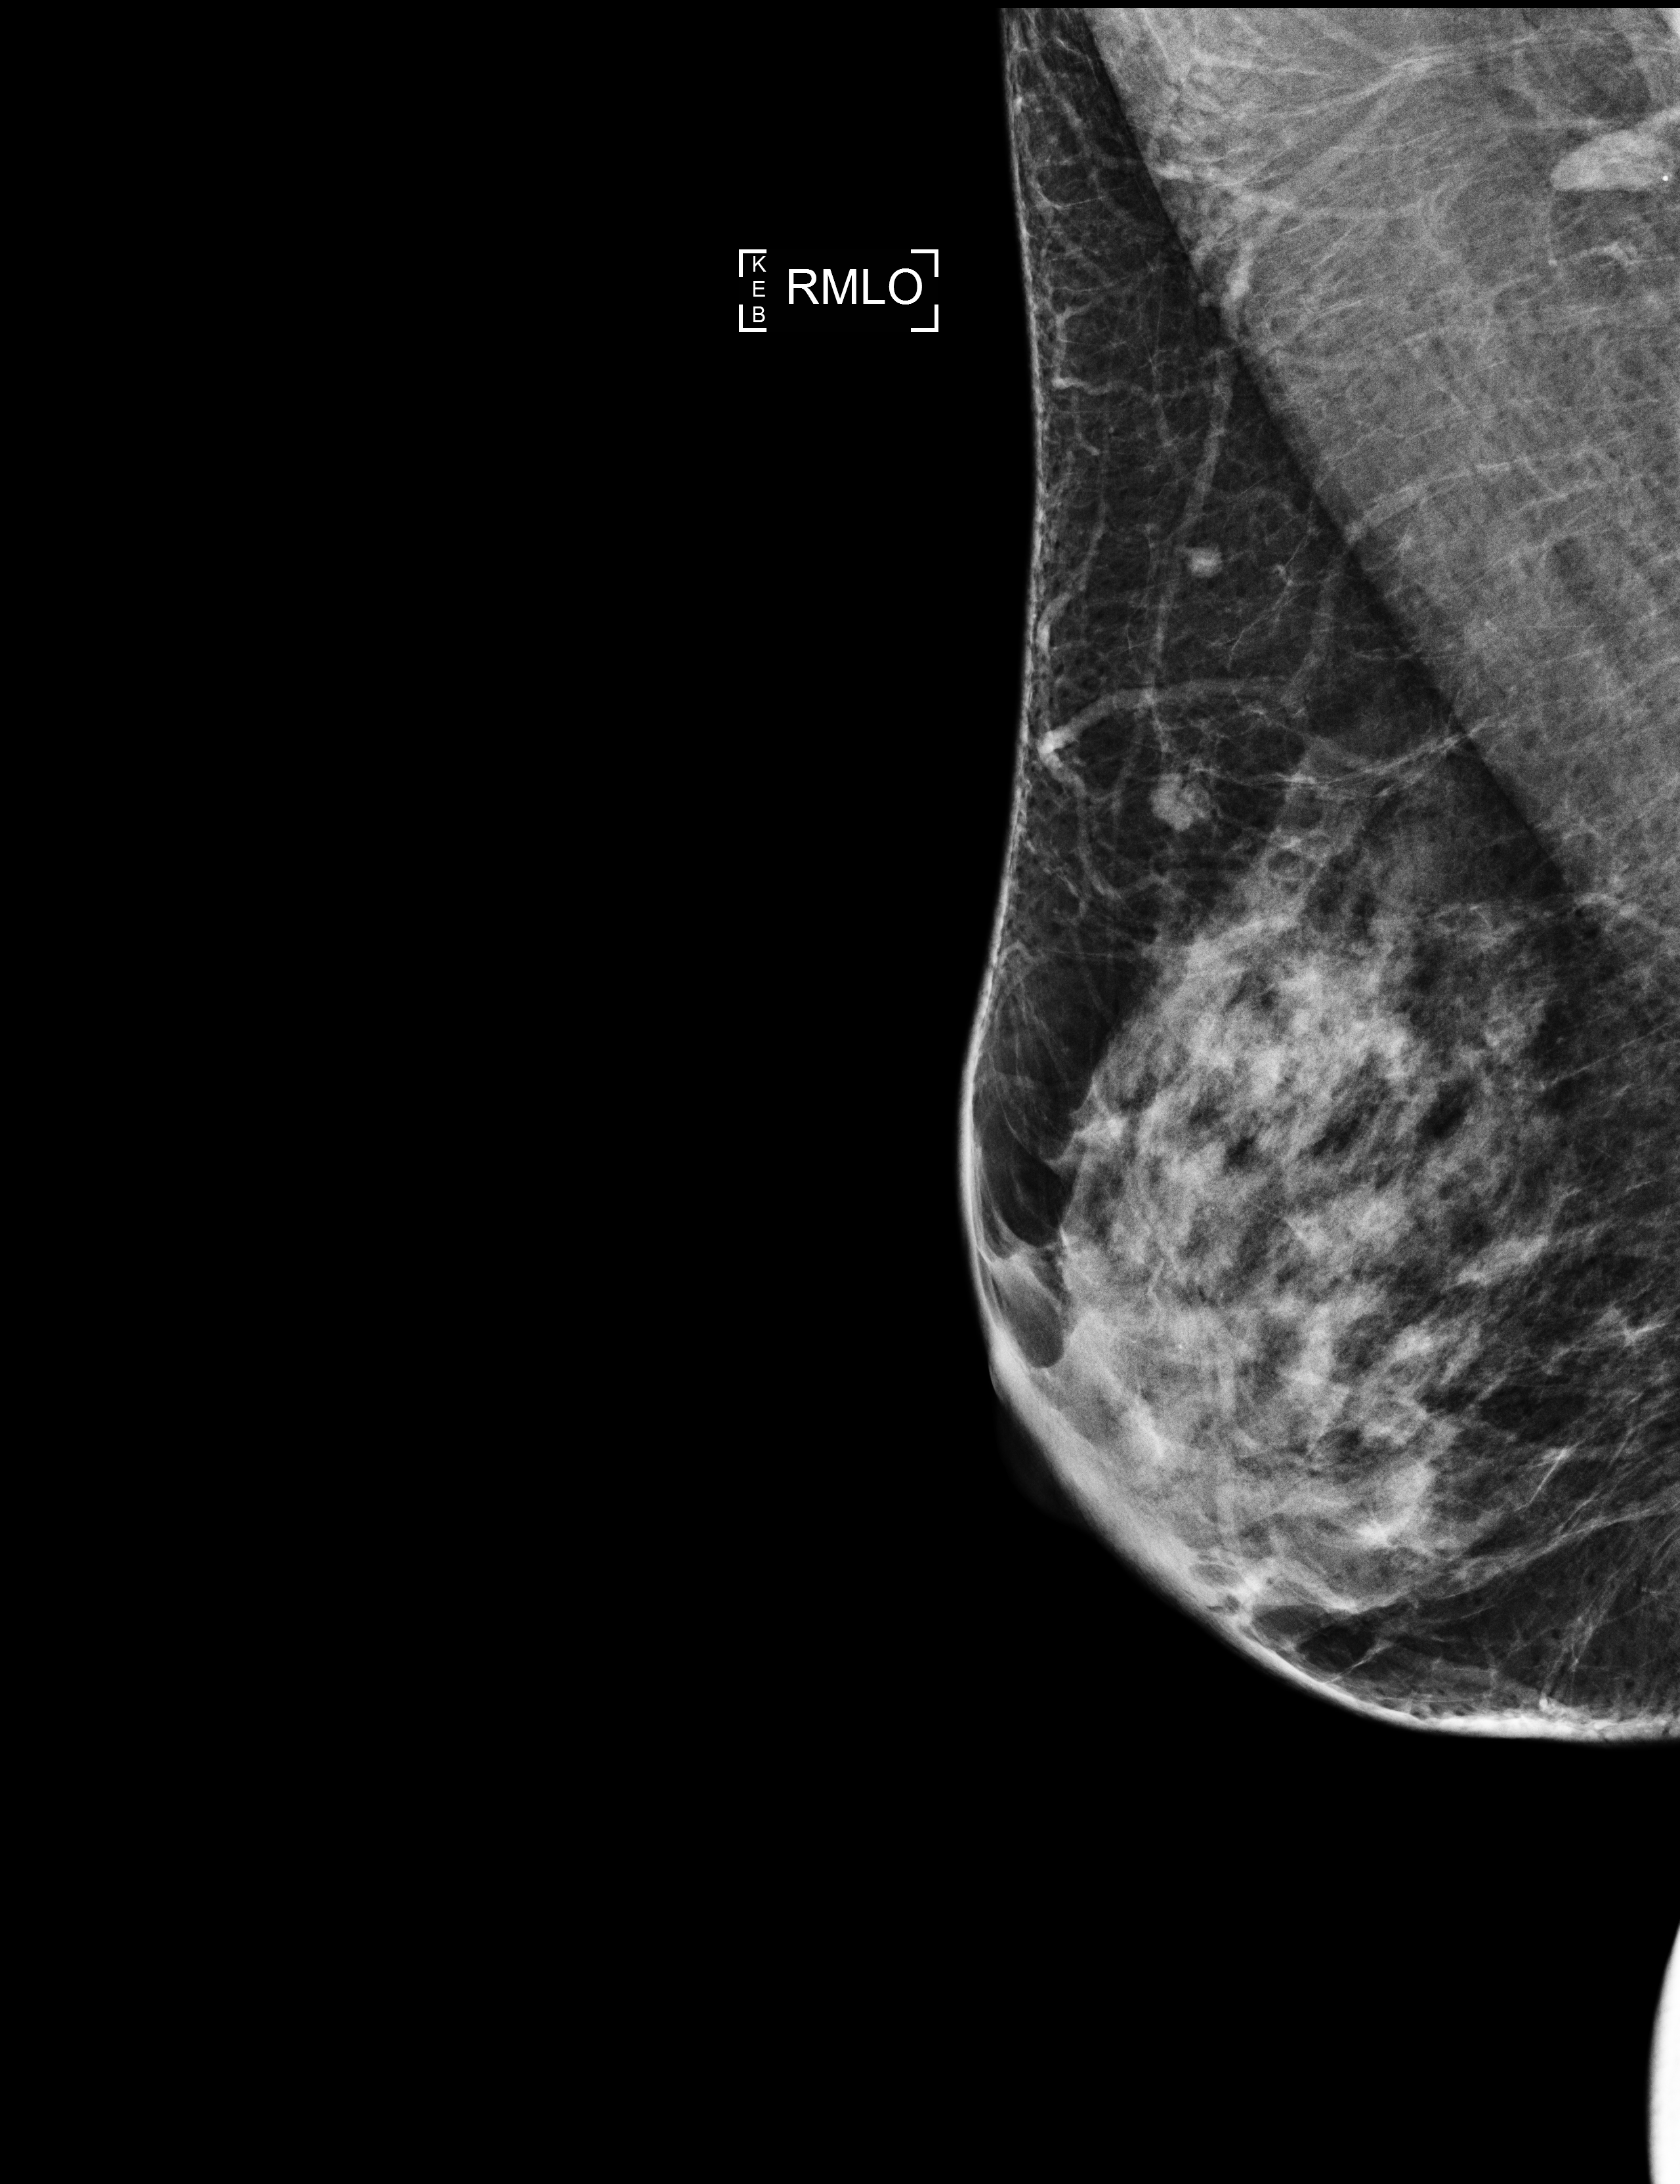
Screening examination, compressed breast thickness 51 mm. Patient aged 44 years (female).
Image type: full-field digital mammogram. Breast: right. Projection: medio-lateral oblique projection. Breast density at the screening exam (both breasts): heterogeneously dense (BI-RADS density category c). Final BI-RADS assessment for this screening round (tomosynthesis exam, both breasts): category 2. Recall: no recall after this screen.